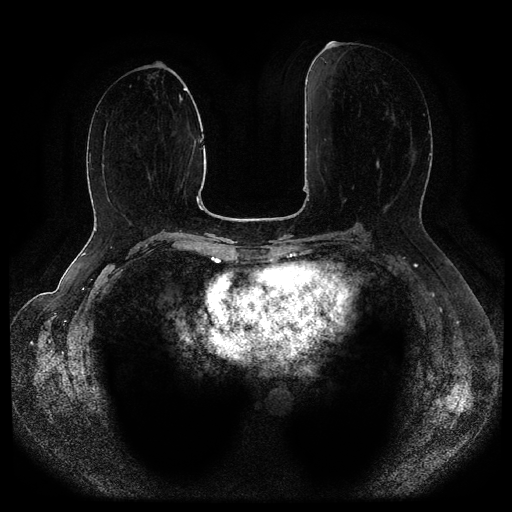
Breast MRI (dynamic contrast-enhanced, multi-phase), one axial slice. Slice 45 of 116 in the series (ordered by position). Dynamic contrast-enhanced series, time point 2 of 5 at this slice position (early post-contrast). 1.5 T. TE 2.6 ms, TR 5.3 ms. 512 × 512 image matrix. Patient: female, 55 years.
Structures marked on this image (semi-automatically segmented with operator editing):
- breast lesion (labelled benign in the annotation): bounding box <376,161,379,168> (left, top, right, bottom; pixels)